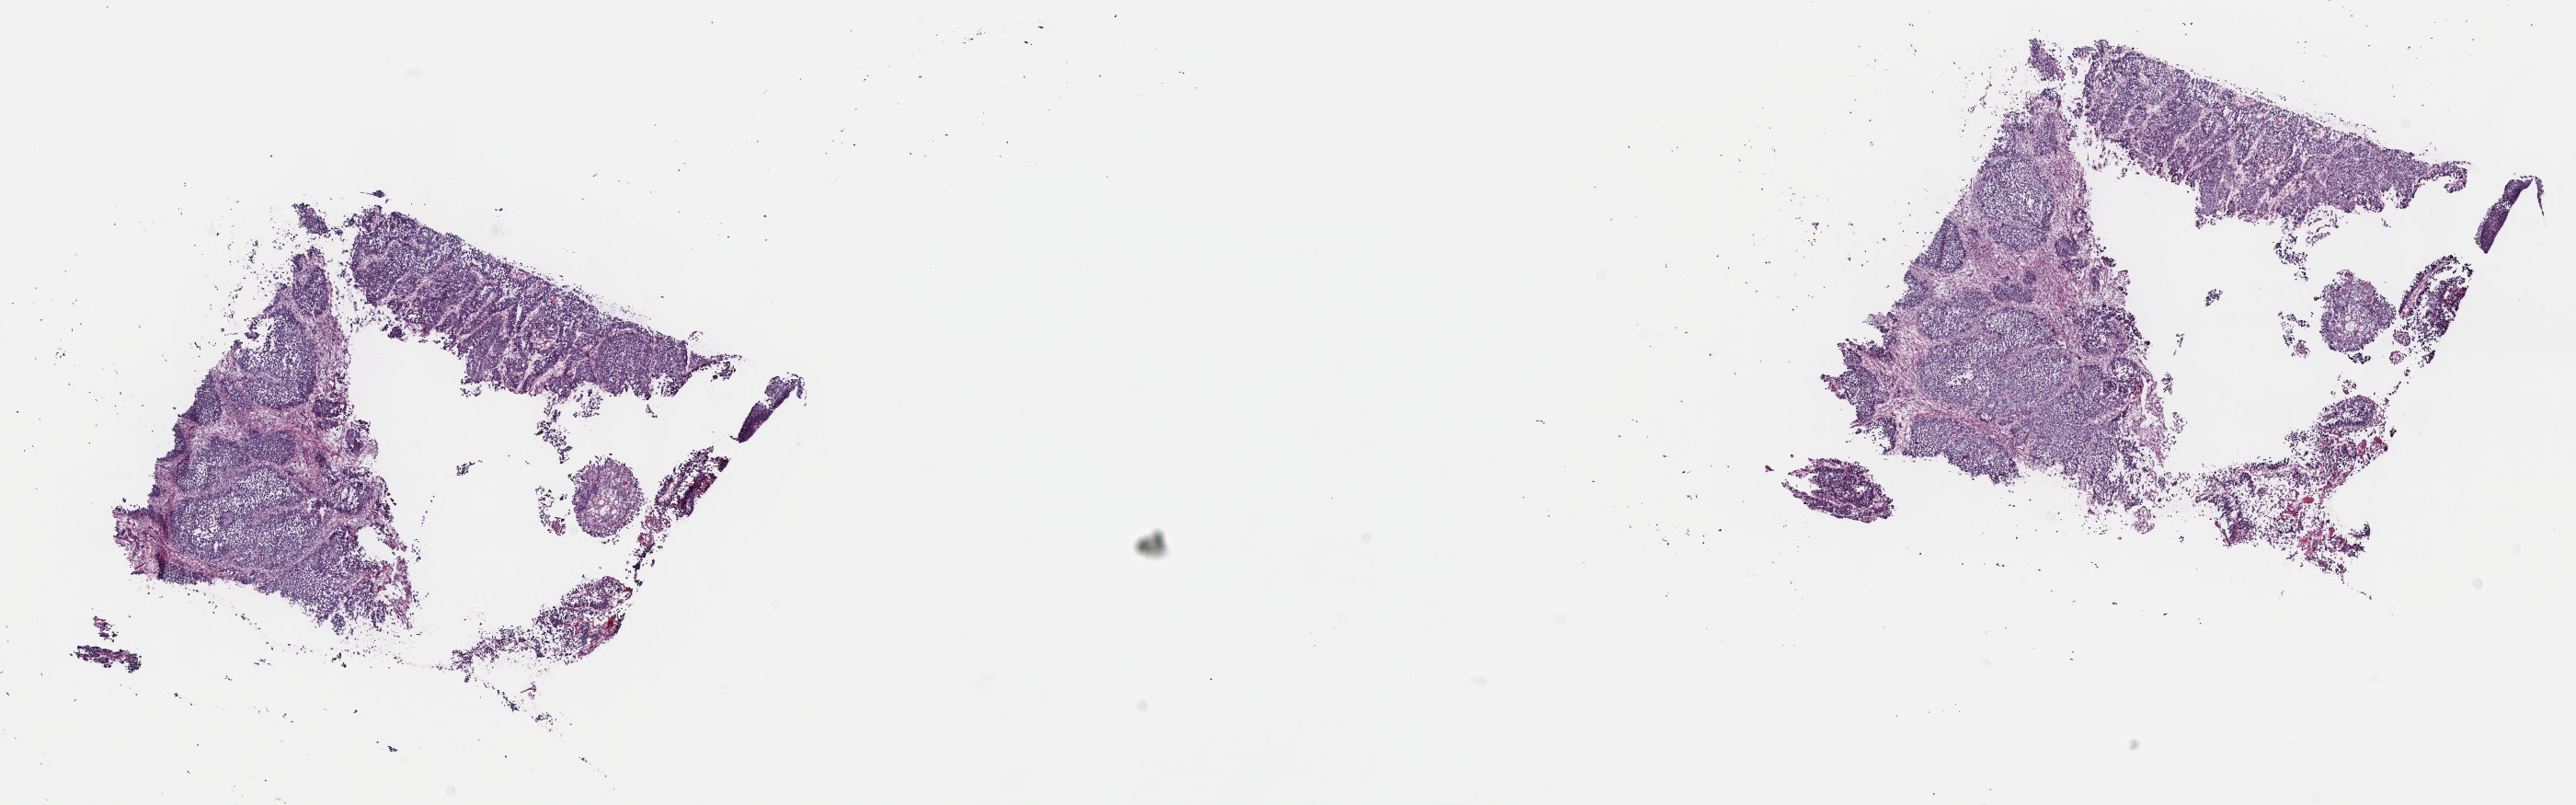
Whole-slide histology image, Hematoxylin and eosin (H&E) stained, whole scanned area (about 22.7 x 7.1 mm, from a 40x scan) shown as a low-resolution overview. Frozen section. Sample: primary tumour, bladder. Female patient; age at initial diagnosis 81 years. Composition of this section per pathologist review: tumour cells 85%, tumour nuclei 85%.
Histologic diagnosis: Papillary transitional cell carcinoma.